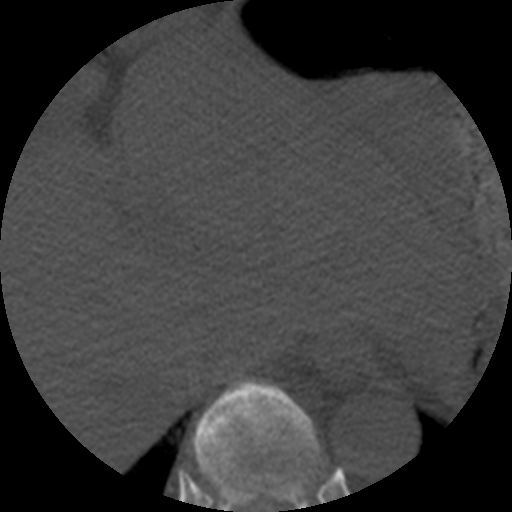
CT including the spine, one axial slice. Slice 276 of 508 in the series (ordered by position). Reconstruction kernel STANDARD. 120 kVp. Bone window (W 1800 / L 400 HU). 512 × 512 image matrix, field of view 160 × 160 mm. Patient age 57 years. Case-level facts recorded for this patient, not image findings: primary cancer: prostate.
Outlined on this slice (semi-automatically segmented with operator editing):
- T10 vertebra: bounding box <193,377,317,512> (left, top, right, bottom; pixels)
- T9 vertebra: <203,446,319,508>